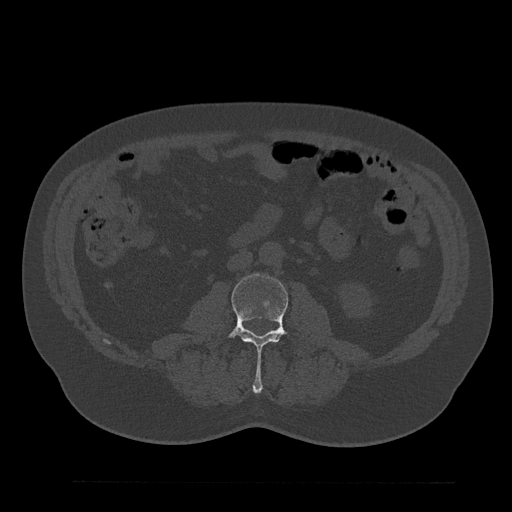
CT including the spine, one axial slice. Position 30 of 797 along the scan axis. Reconstruction kernel Br40s/3. Bone window (W 1800 / L 400 HU). 0.5 mm slice thickness. 512 × 512 image matrix. Patient: male, 61 years. Case-level facts recorded for this patient, not image findings: primary cancer: prostate.
Structures marked on this image (semi-automatically segmented with operator editing):
- L3 vertebra: bounding box [x1, y1, x2, y2] px = [224, 274, 318, 393]